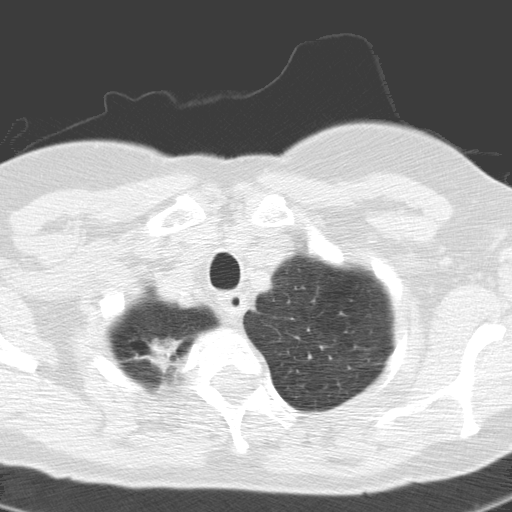
Low-dose screening chest CT, axial slice. Baseline screening round. Lung window (W 1500 / L -600 HU). 3.2 mm slice thickness. Slice 11 of 155 in the series. Female participant, aged 60 years at enrolment. Current smoker at enrolment.
- Lesion marked by an expert reader, bounding box (x1, y1, x2, y2) in pixels: (116, 319, 198, 387).
- Screening reader's record for this exam: no non-calcified nodule ≥4 mm recorded.
- Official screen result: negative screen, minor abnormalities not suspicious for lung cancer.
- Lung cancer was diagnosed 391 days after this screen: squamous cell carcinoma, keratinizing, NOS, right upper lobe, moderately differentiated (G2), stage IA (AJCC 6th edition), 20 mm at pathology.